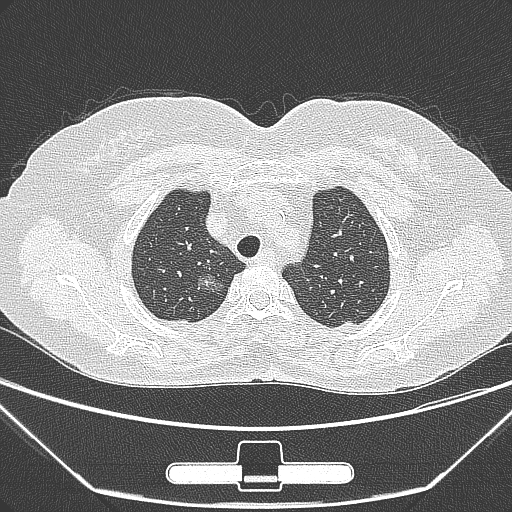
Chest CT, one axial slice. Position 229 of 275 along the scan axis. Lung window (W 1500 / L -600 HU). 512 × 512 image matrix, field of view 356 × 356 mm. Patient: female, 63 years. From the clinical record (not read from this slice): clinical TNM (as recorded): T1a N0 M0; histopathological grade: G1.
Outlined on this slice (rectangle marked by the reading radiologist):
- lung tumour (recorded histology: adenocarcinoma): bounding box <192,265,226,300> (left, top, right, bottom; pixels)